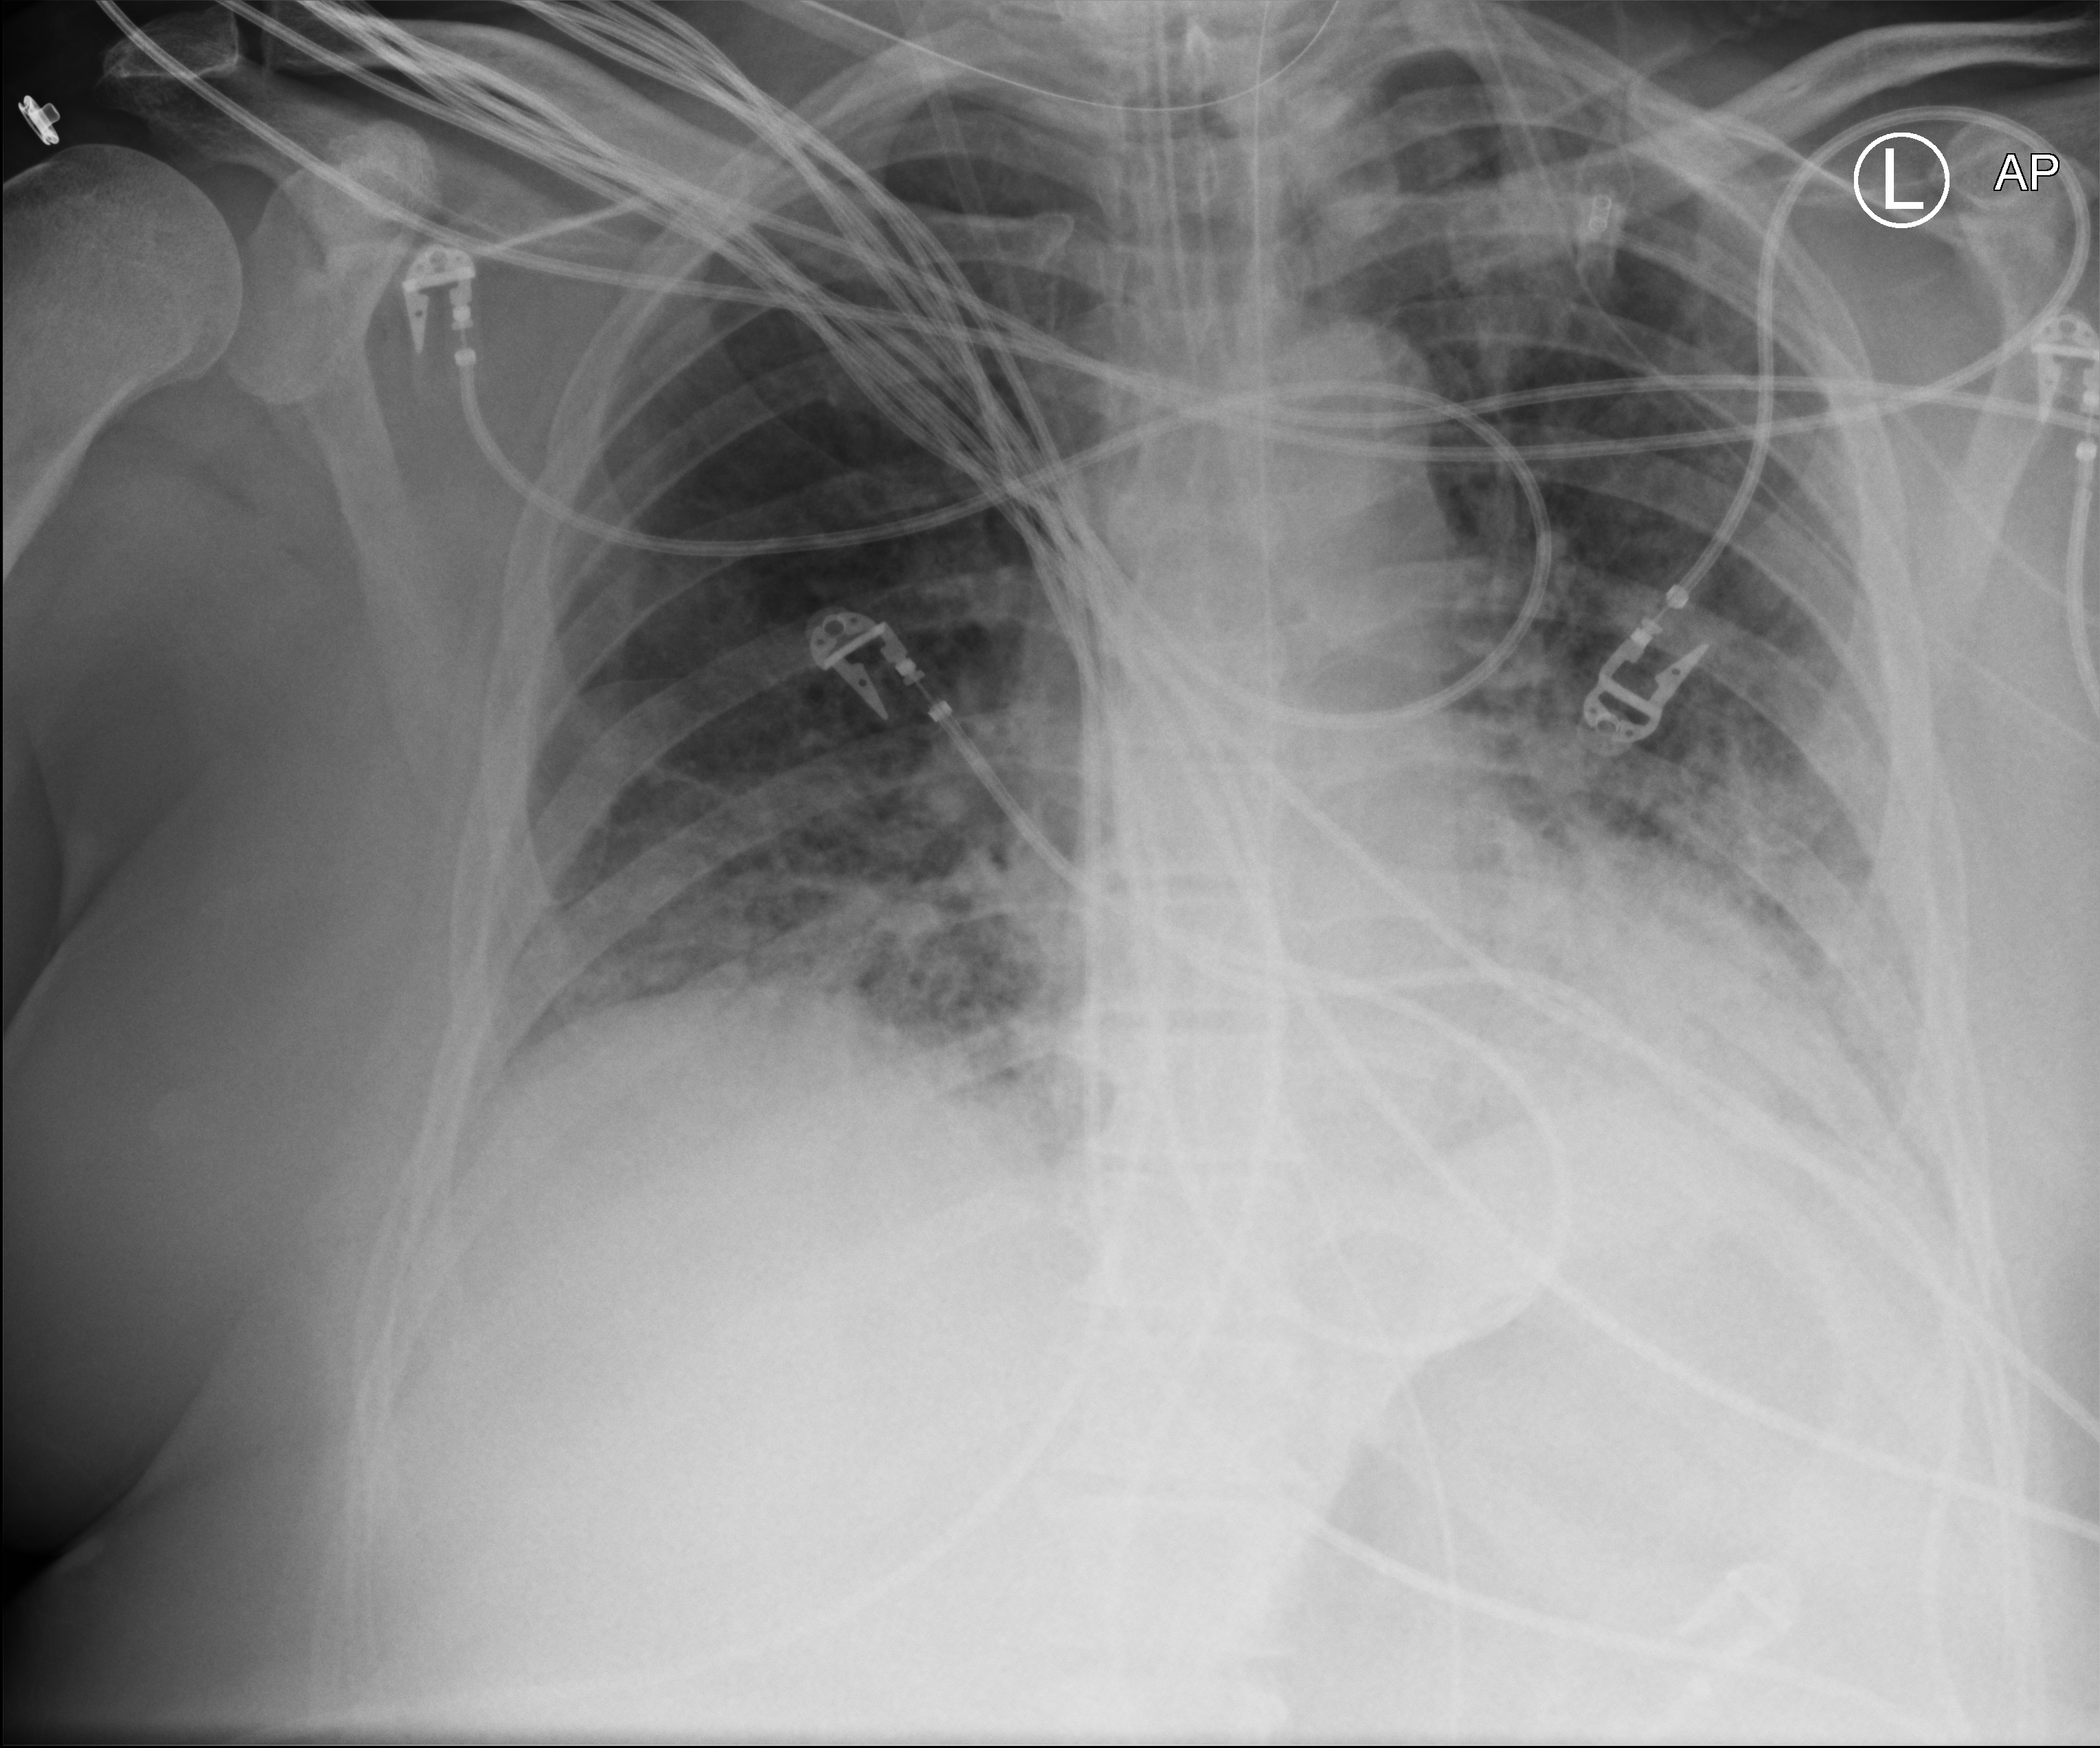
Portable chest radiograph, anteroposterior (AP) projection. Male patient hospitalised with COVID-19, age 60–74 years.
Hospital-stay facts (about this admission, not read from this image; timing relative to this image not recorded):
- diabetes (admission record): no